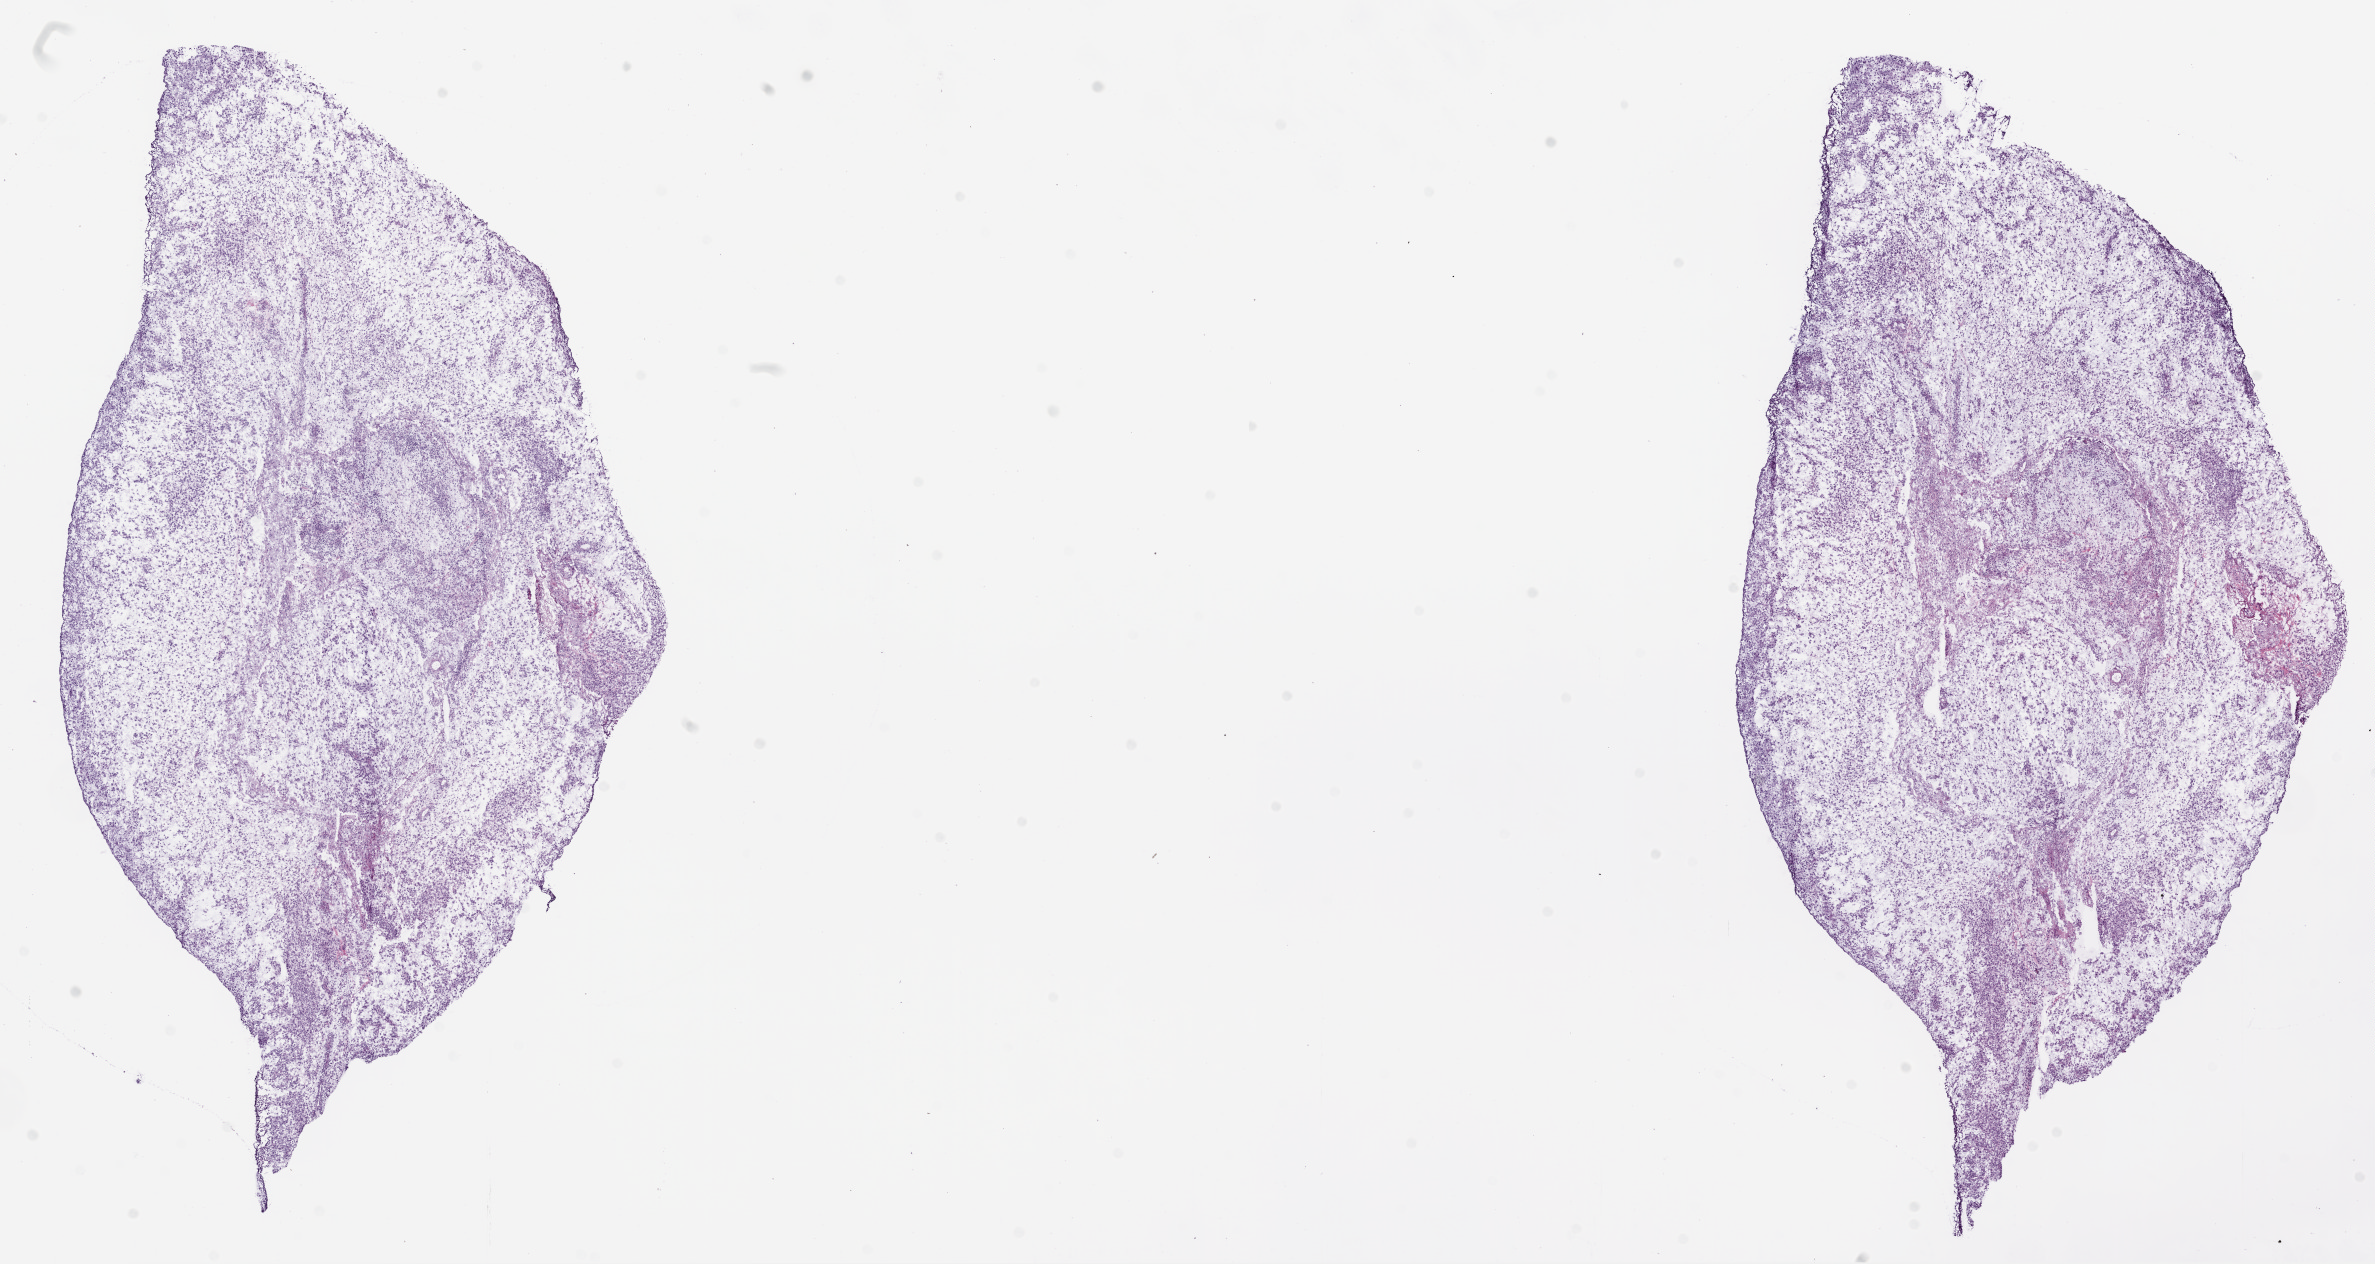
Whole-slide histology image, Hematoxylin and eosin (H&E) stained, a low-resolution overview of the entire scanned area, about 19.1 x 10.1 mm (from a 20x scan). Frozen section. Brain, primary tumour sample. Patient: male, age at initial diagnosis 63 years. Slide review estimates, as recorded: tumour cells 90%, tumour nuclei 80%, normal cells 0%, stromal cells 5%, necrosis 5%.
- histologic diagnosis: Glioblastoma